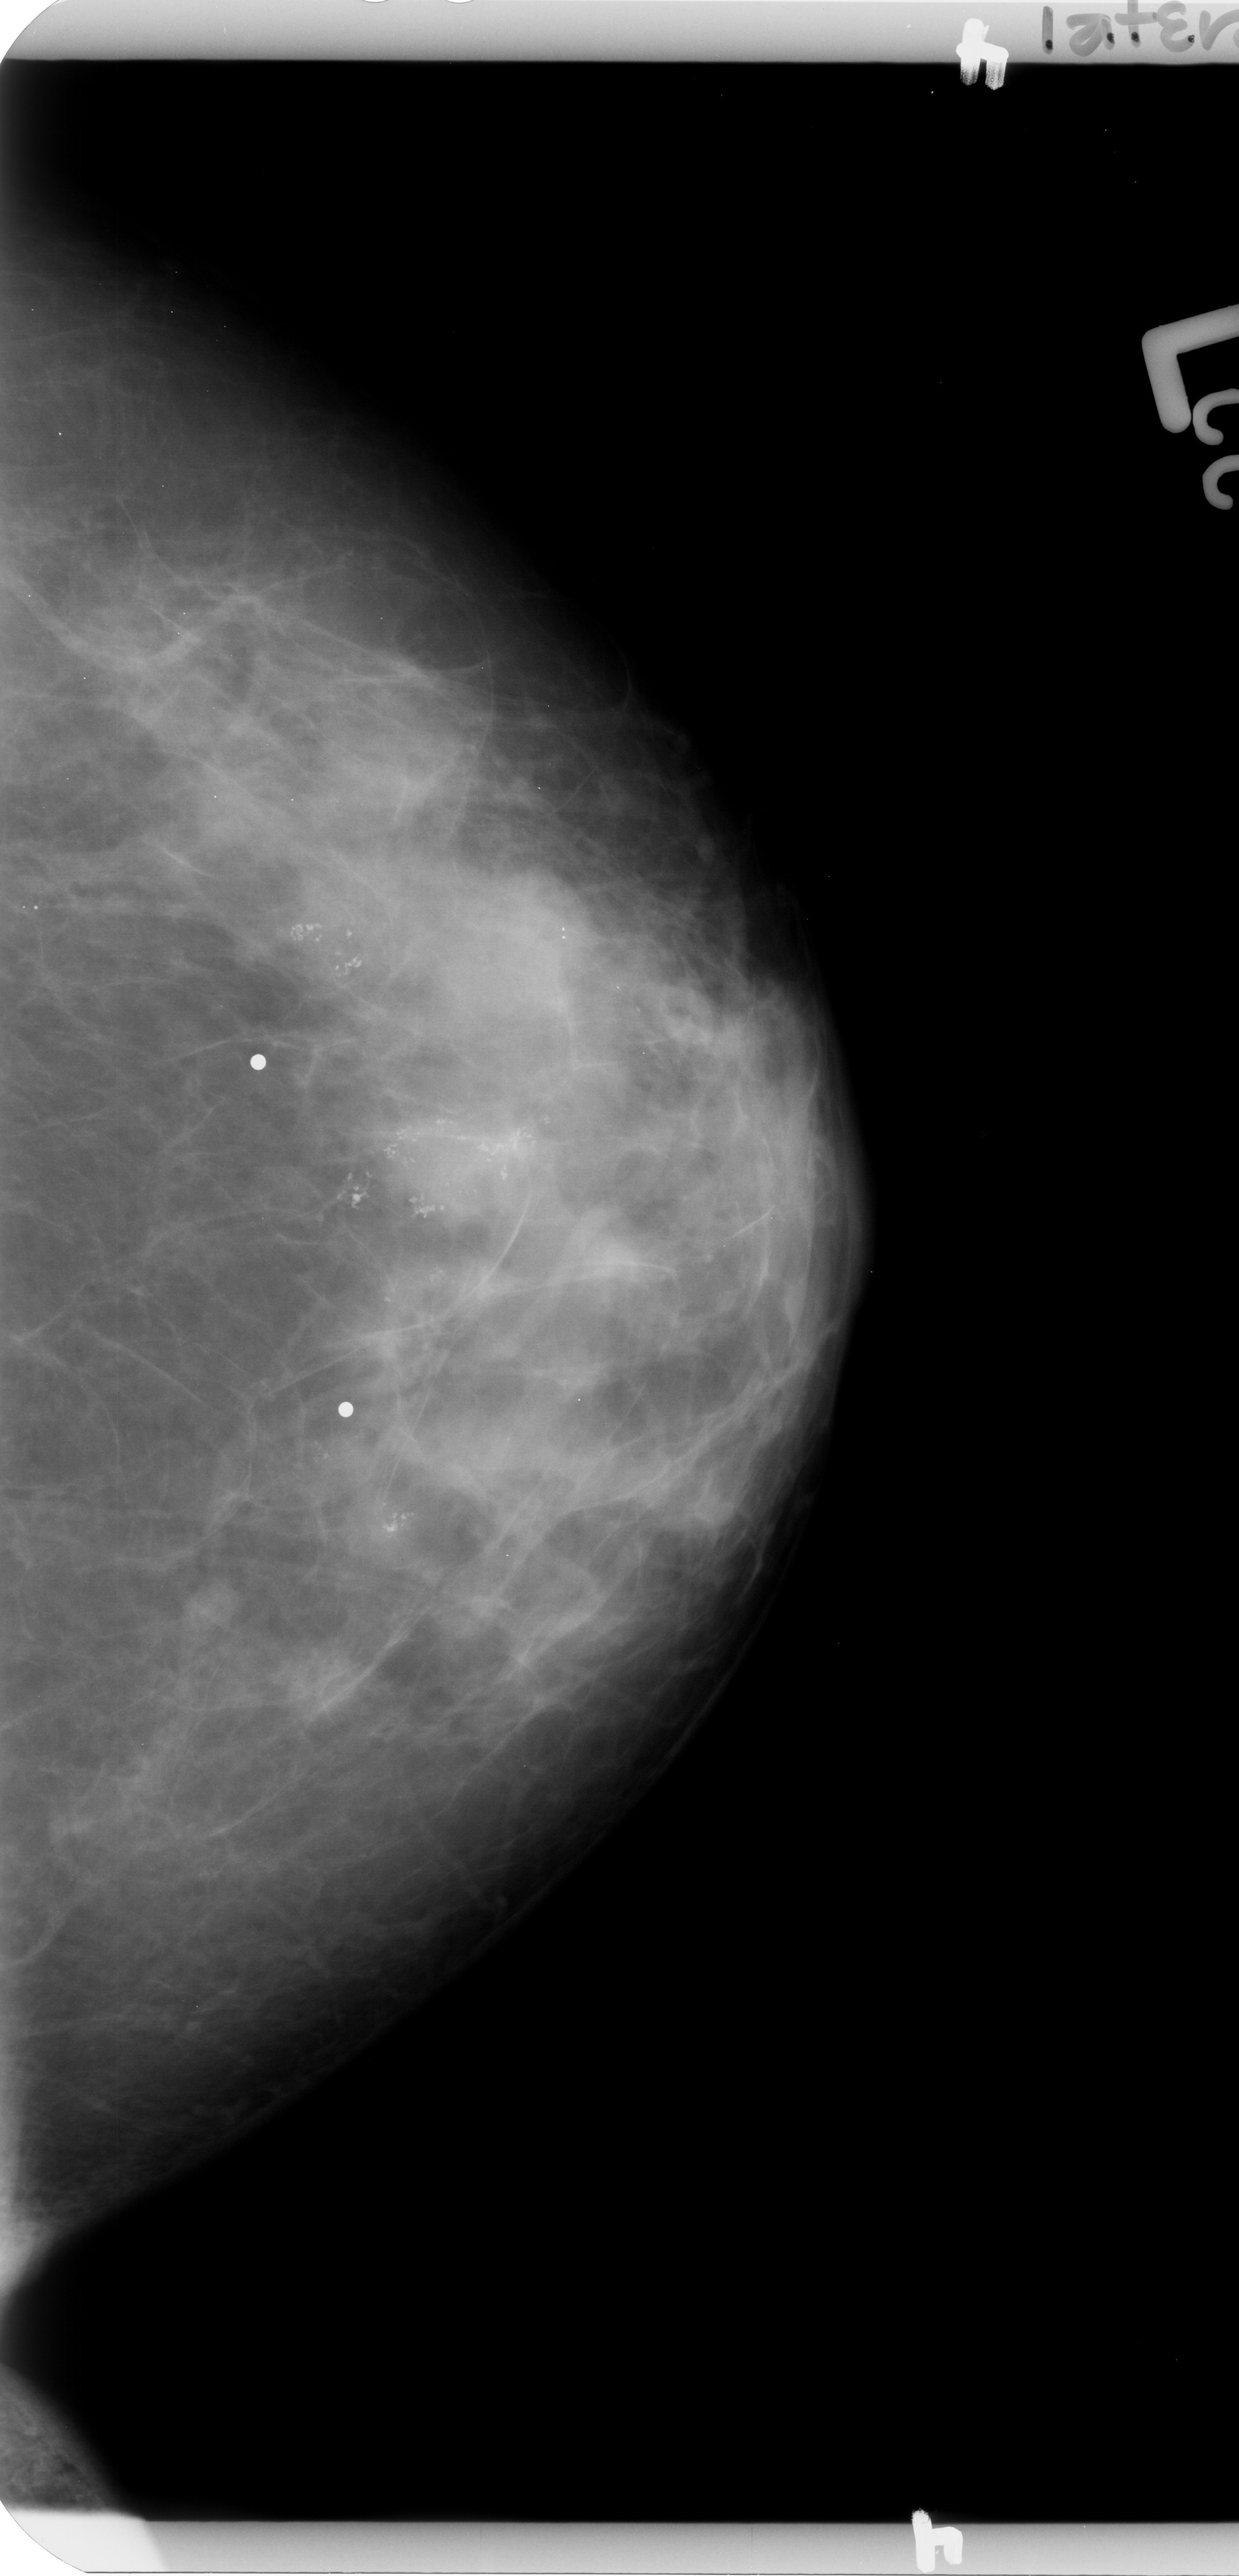
Scanned film-screen mammogram; left breast; CC view; breast composition: heterogeneously dense (BI-RADS density category 3 of 4).
Radiologist-marked abnormalities on this image: Finding 1 of 3: calcifications, morphology pleomorphic, distribution clustered / segmental; BI-RADS assessment category 4; subtlety rating 4 on a 1 (subtle) to 5 (obvious) scale; pathology result (as recorded, not read from the image): benign. Finding 2 of 3: calcifications, morphology pleomorphic, distribution clustered / segmental; BI-RADS assessment category 4; pathology (as recorded): benign. Finding 3 of 3: calcifications, morphology pleomorphic, distribution clustered / segmental; BI-RADS assessment category 4; pathology (as recorded): benign.